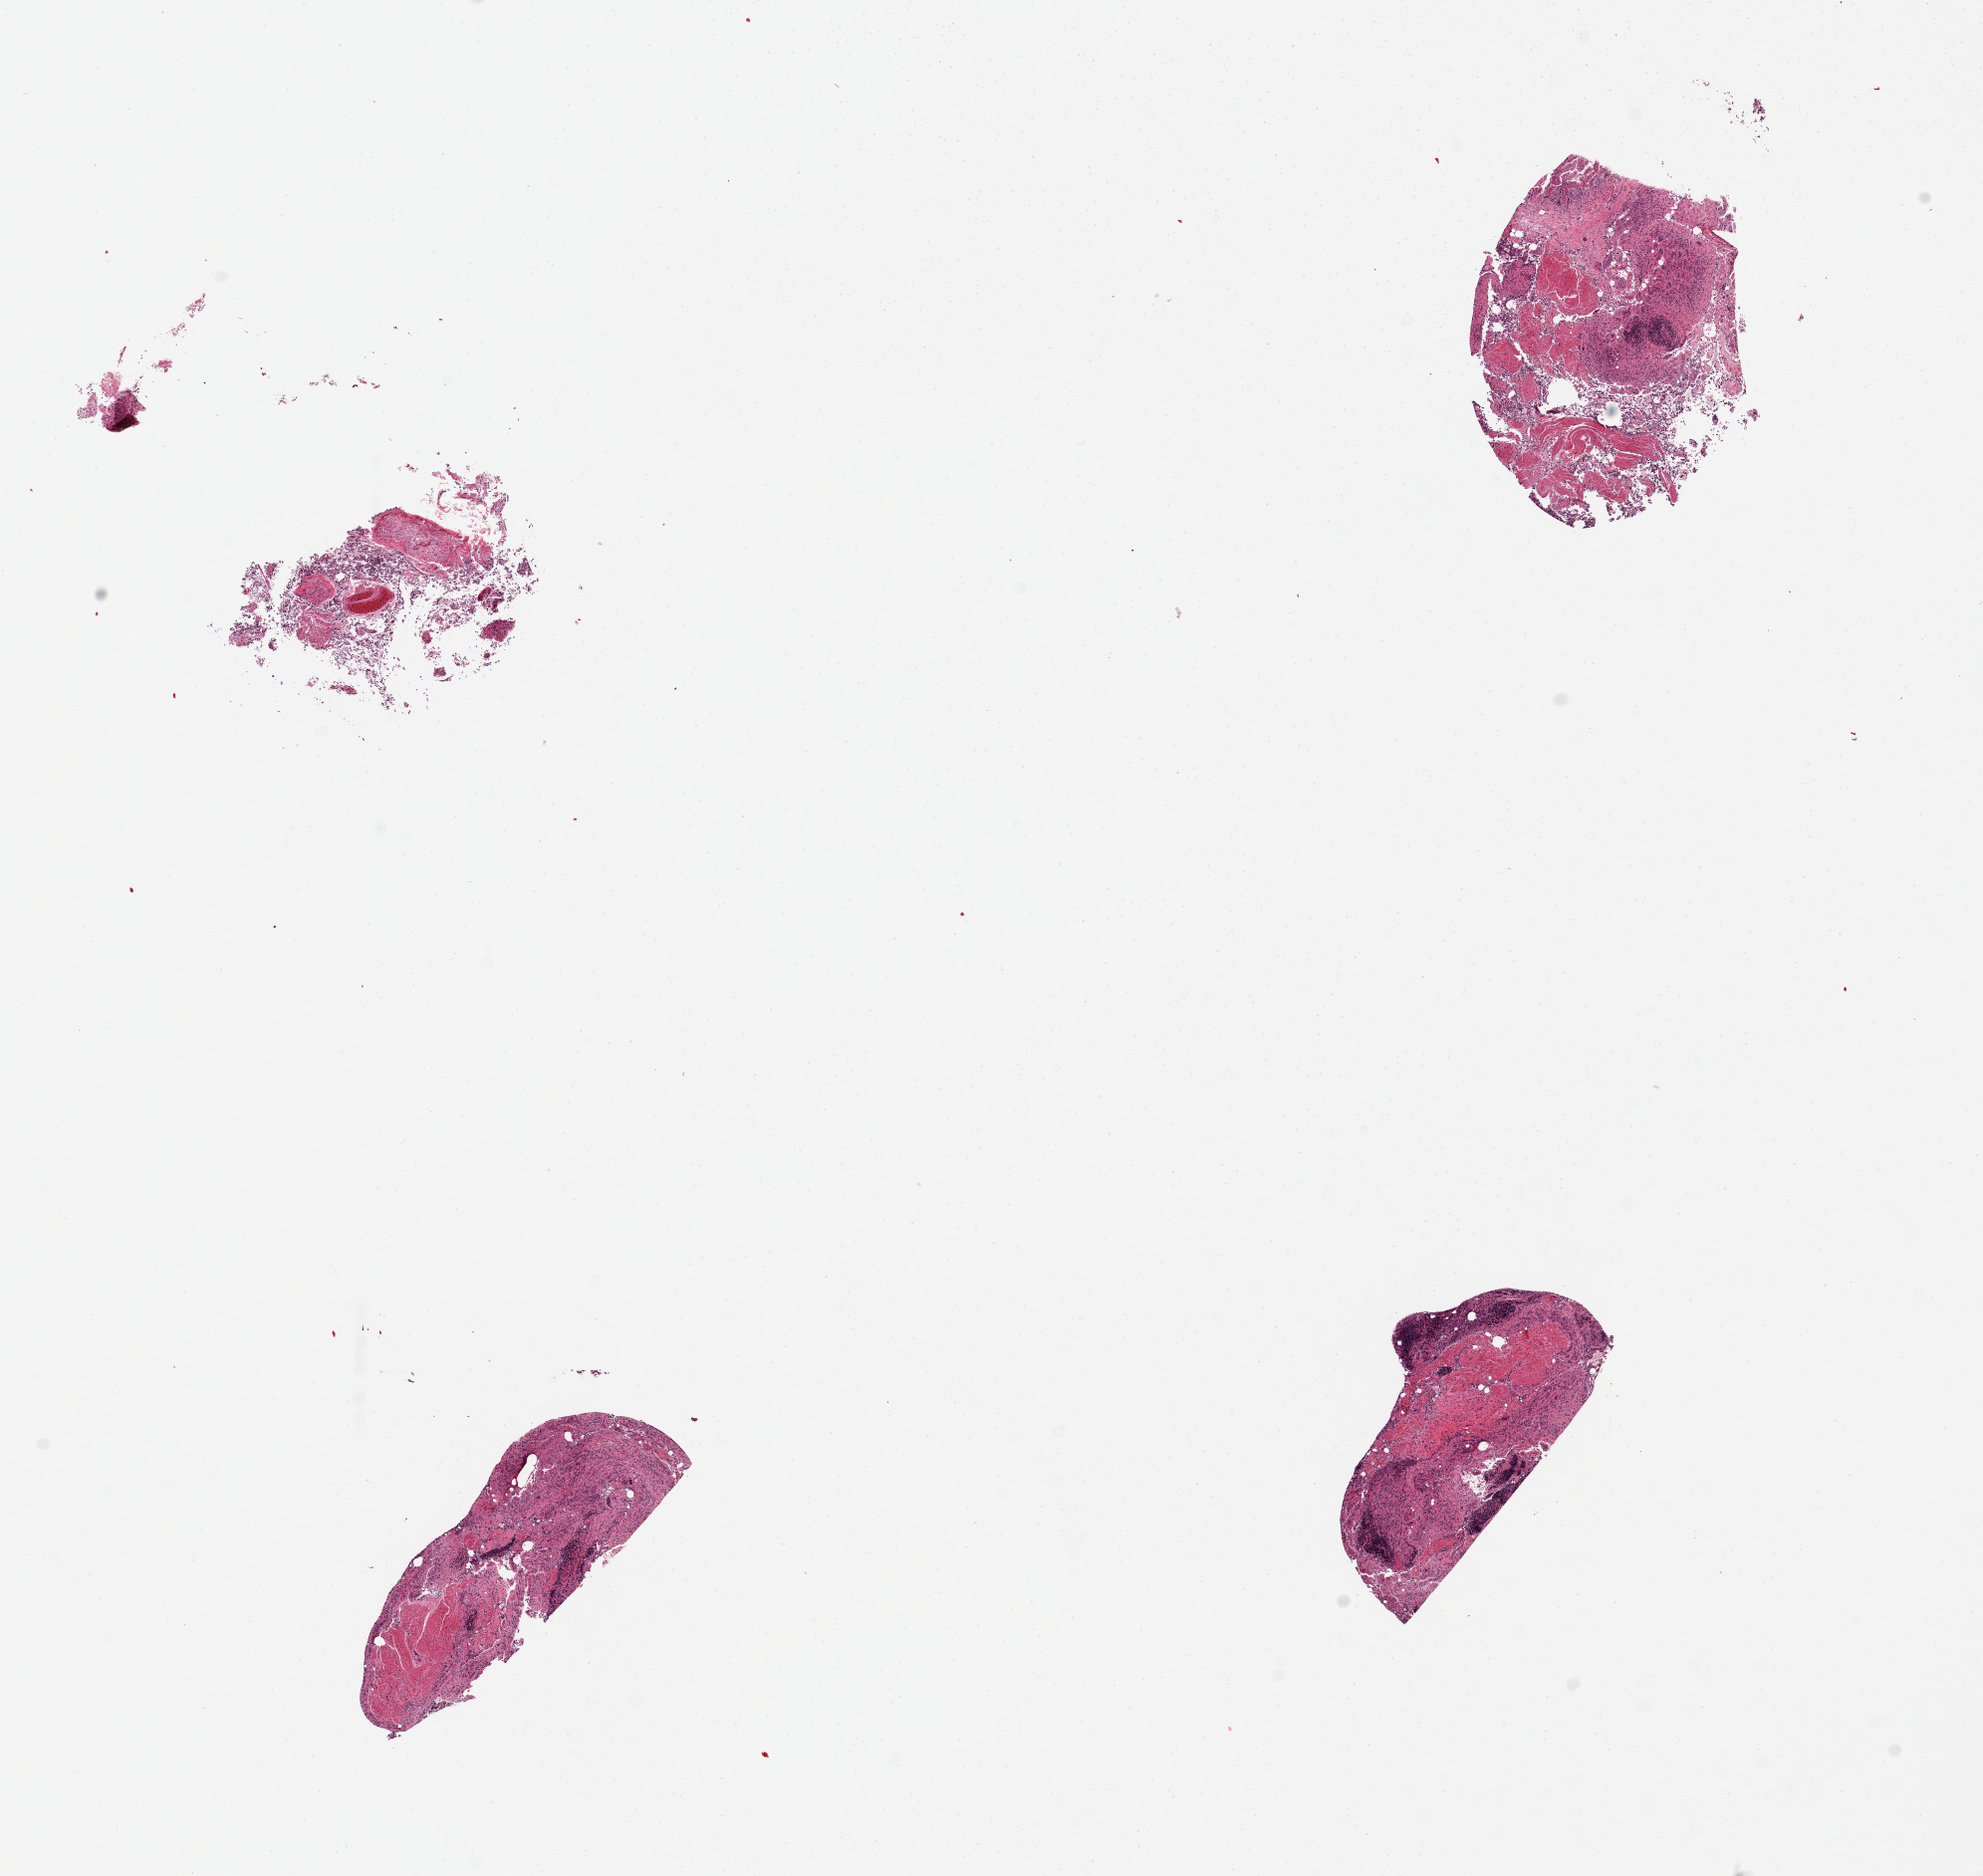
H&E whole-slide image, a low-resolution overview of the entire scanned area, about 15.8 x 14.9 mm; PAXgene-fixed paraffin-embedded (PFPE) section; section of ileum (target tissue); tissue donor sample. Donor: female.
- reviewer comment on this tissue sample: 4 pieces, mainly badly autolyzed mucosa; ~10% lymphoid elements